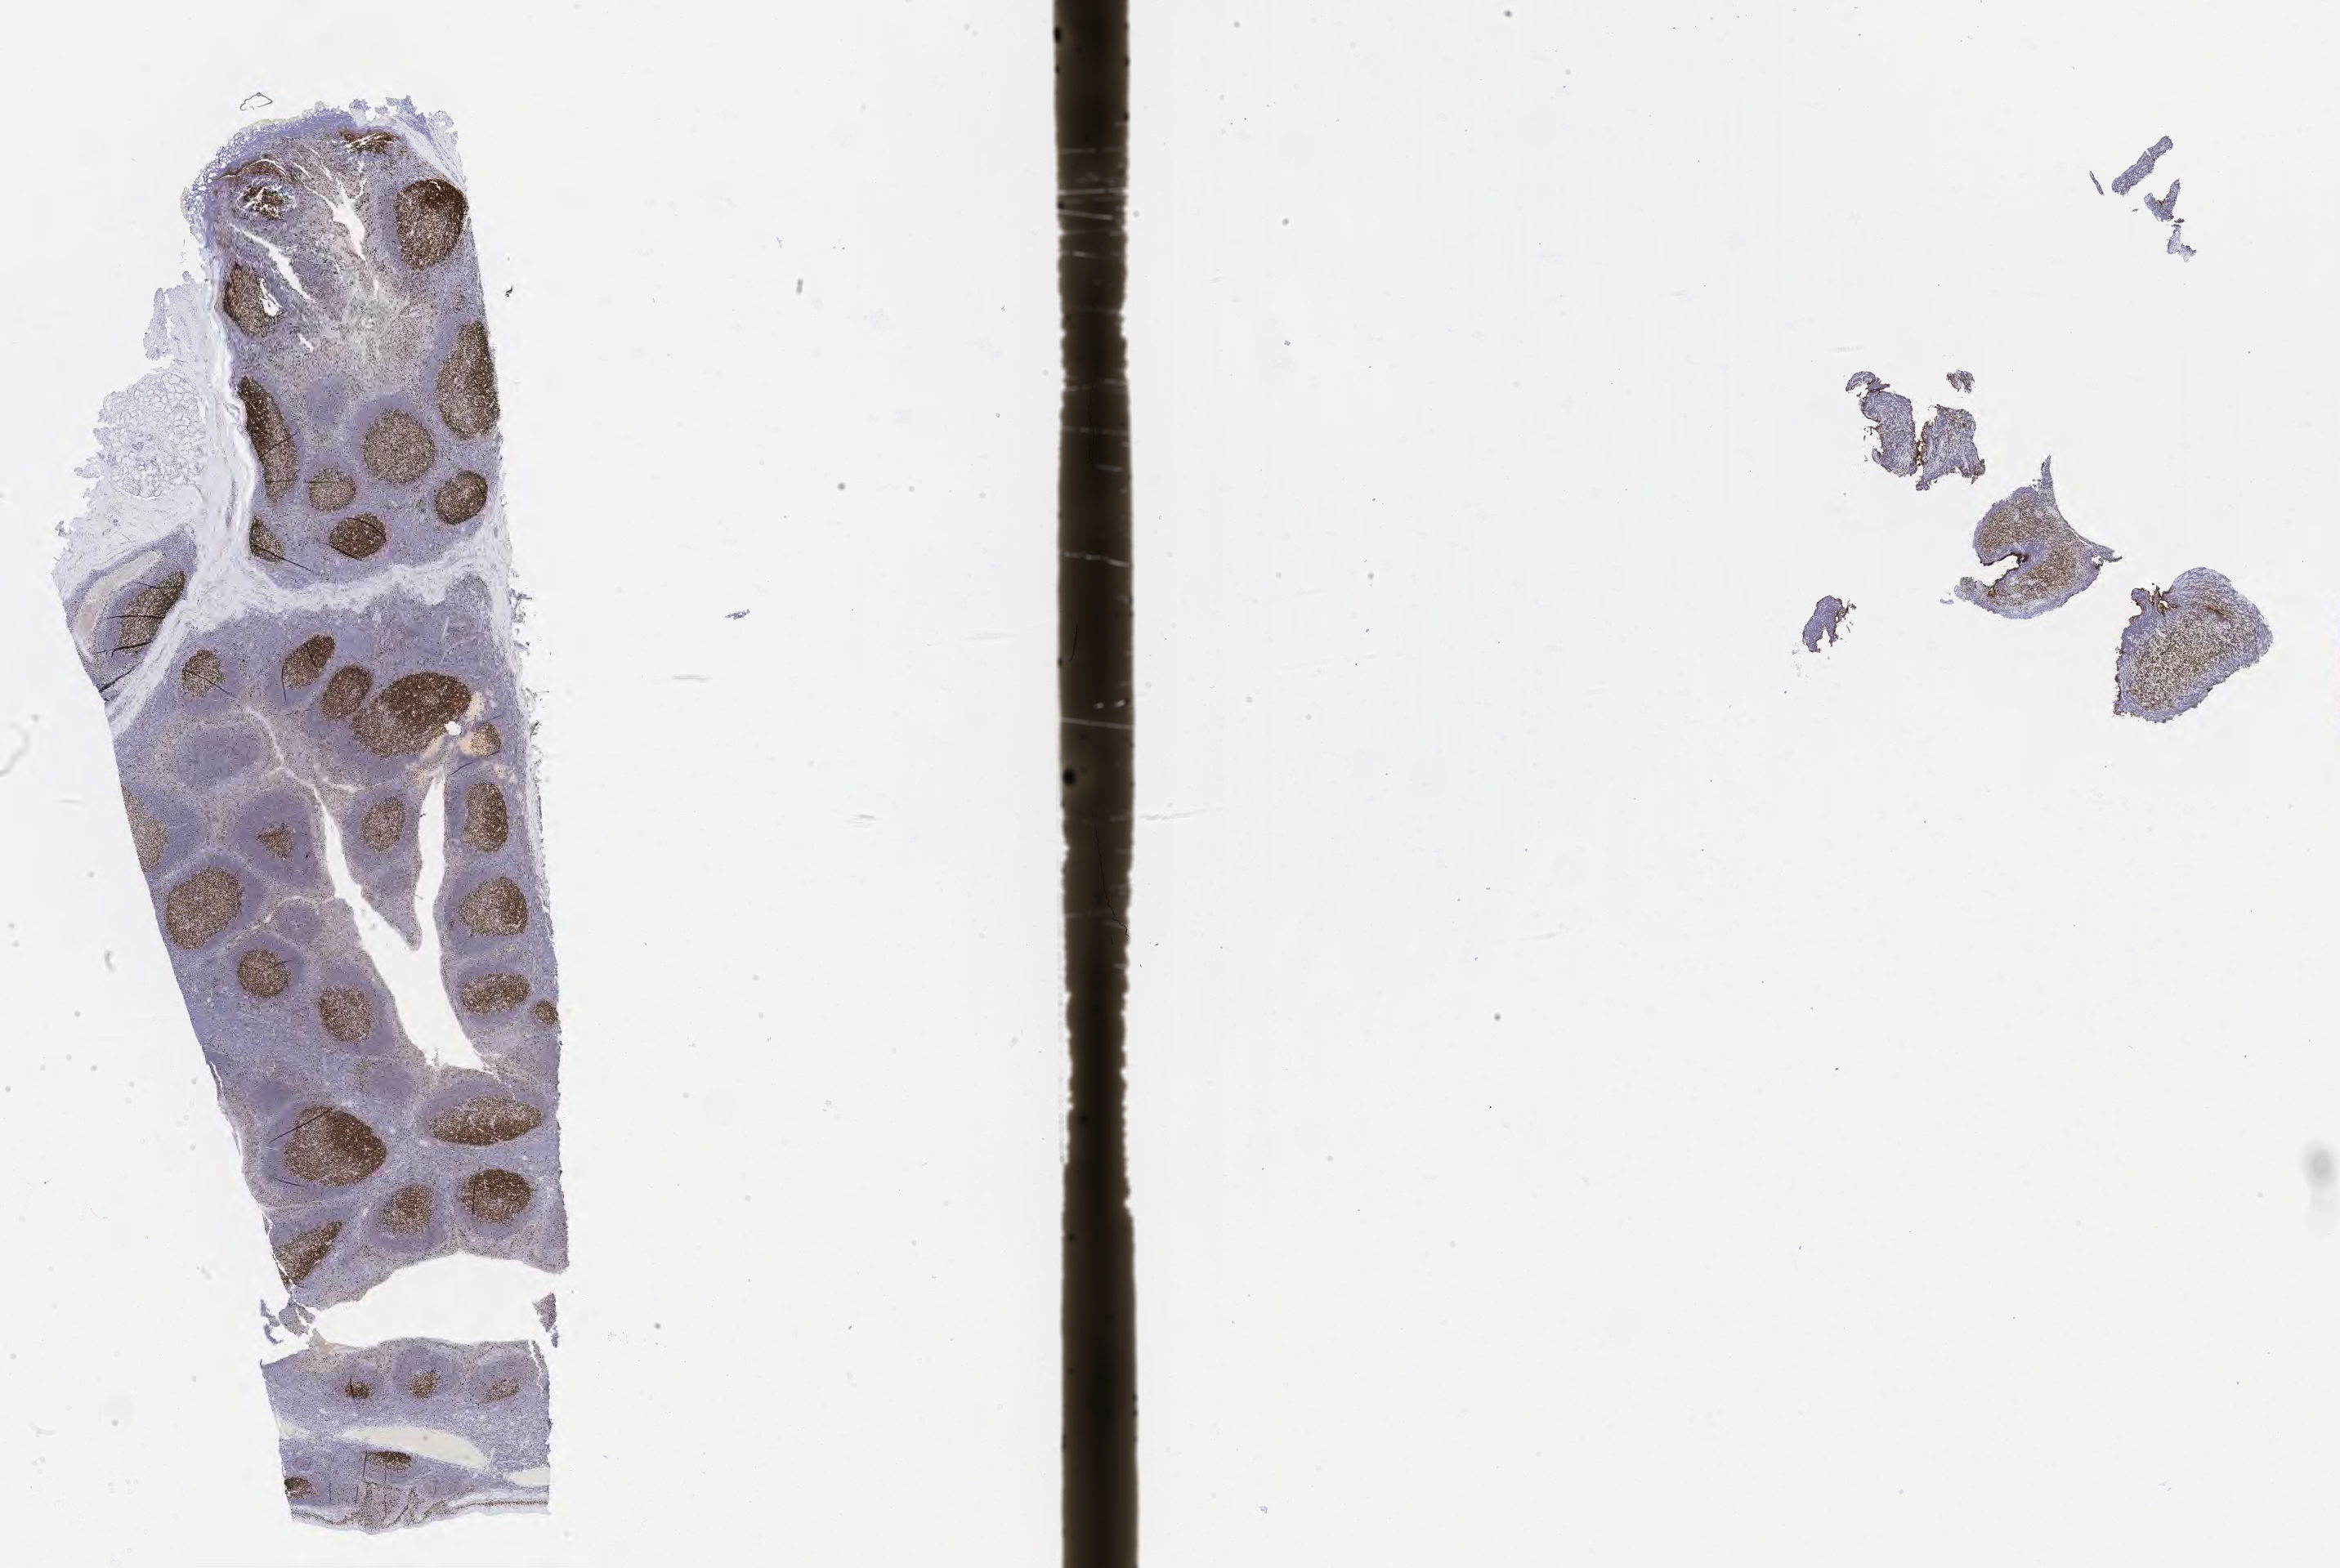
IHC for Ki-67, whole-slide image, a low-resolution overview of the entire scanned area, about 23.1 x 15.5 mm, tumor tissue, site: small intestine. Female patient, 47 years old.
- diagnosis: Burkitt lymphoma, NOS